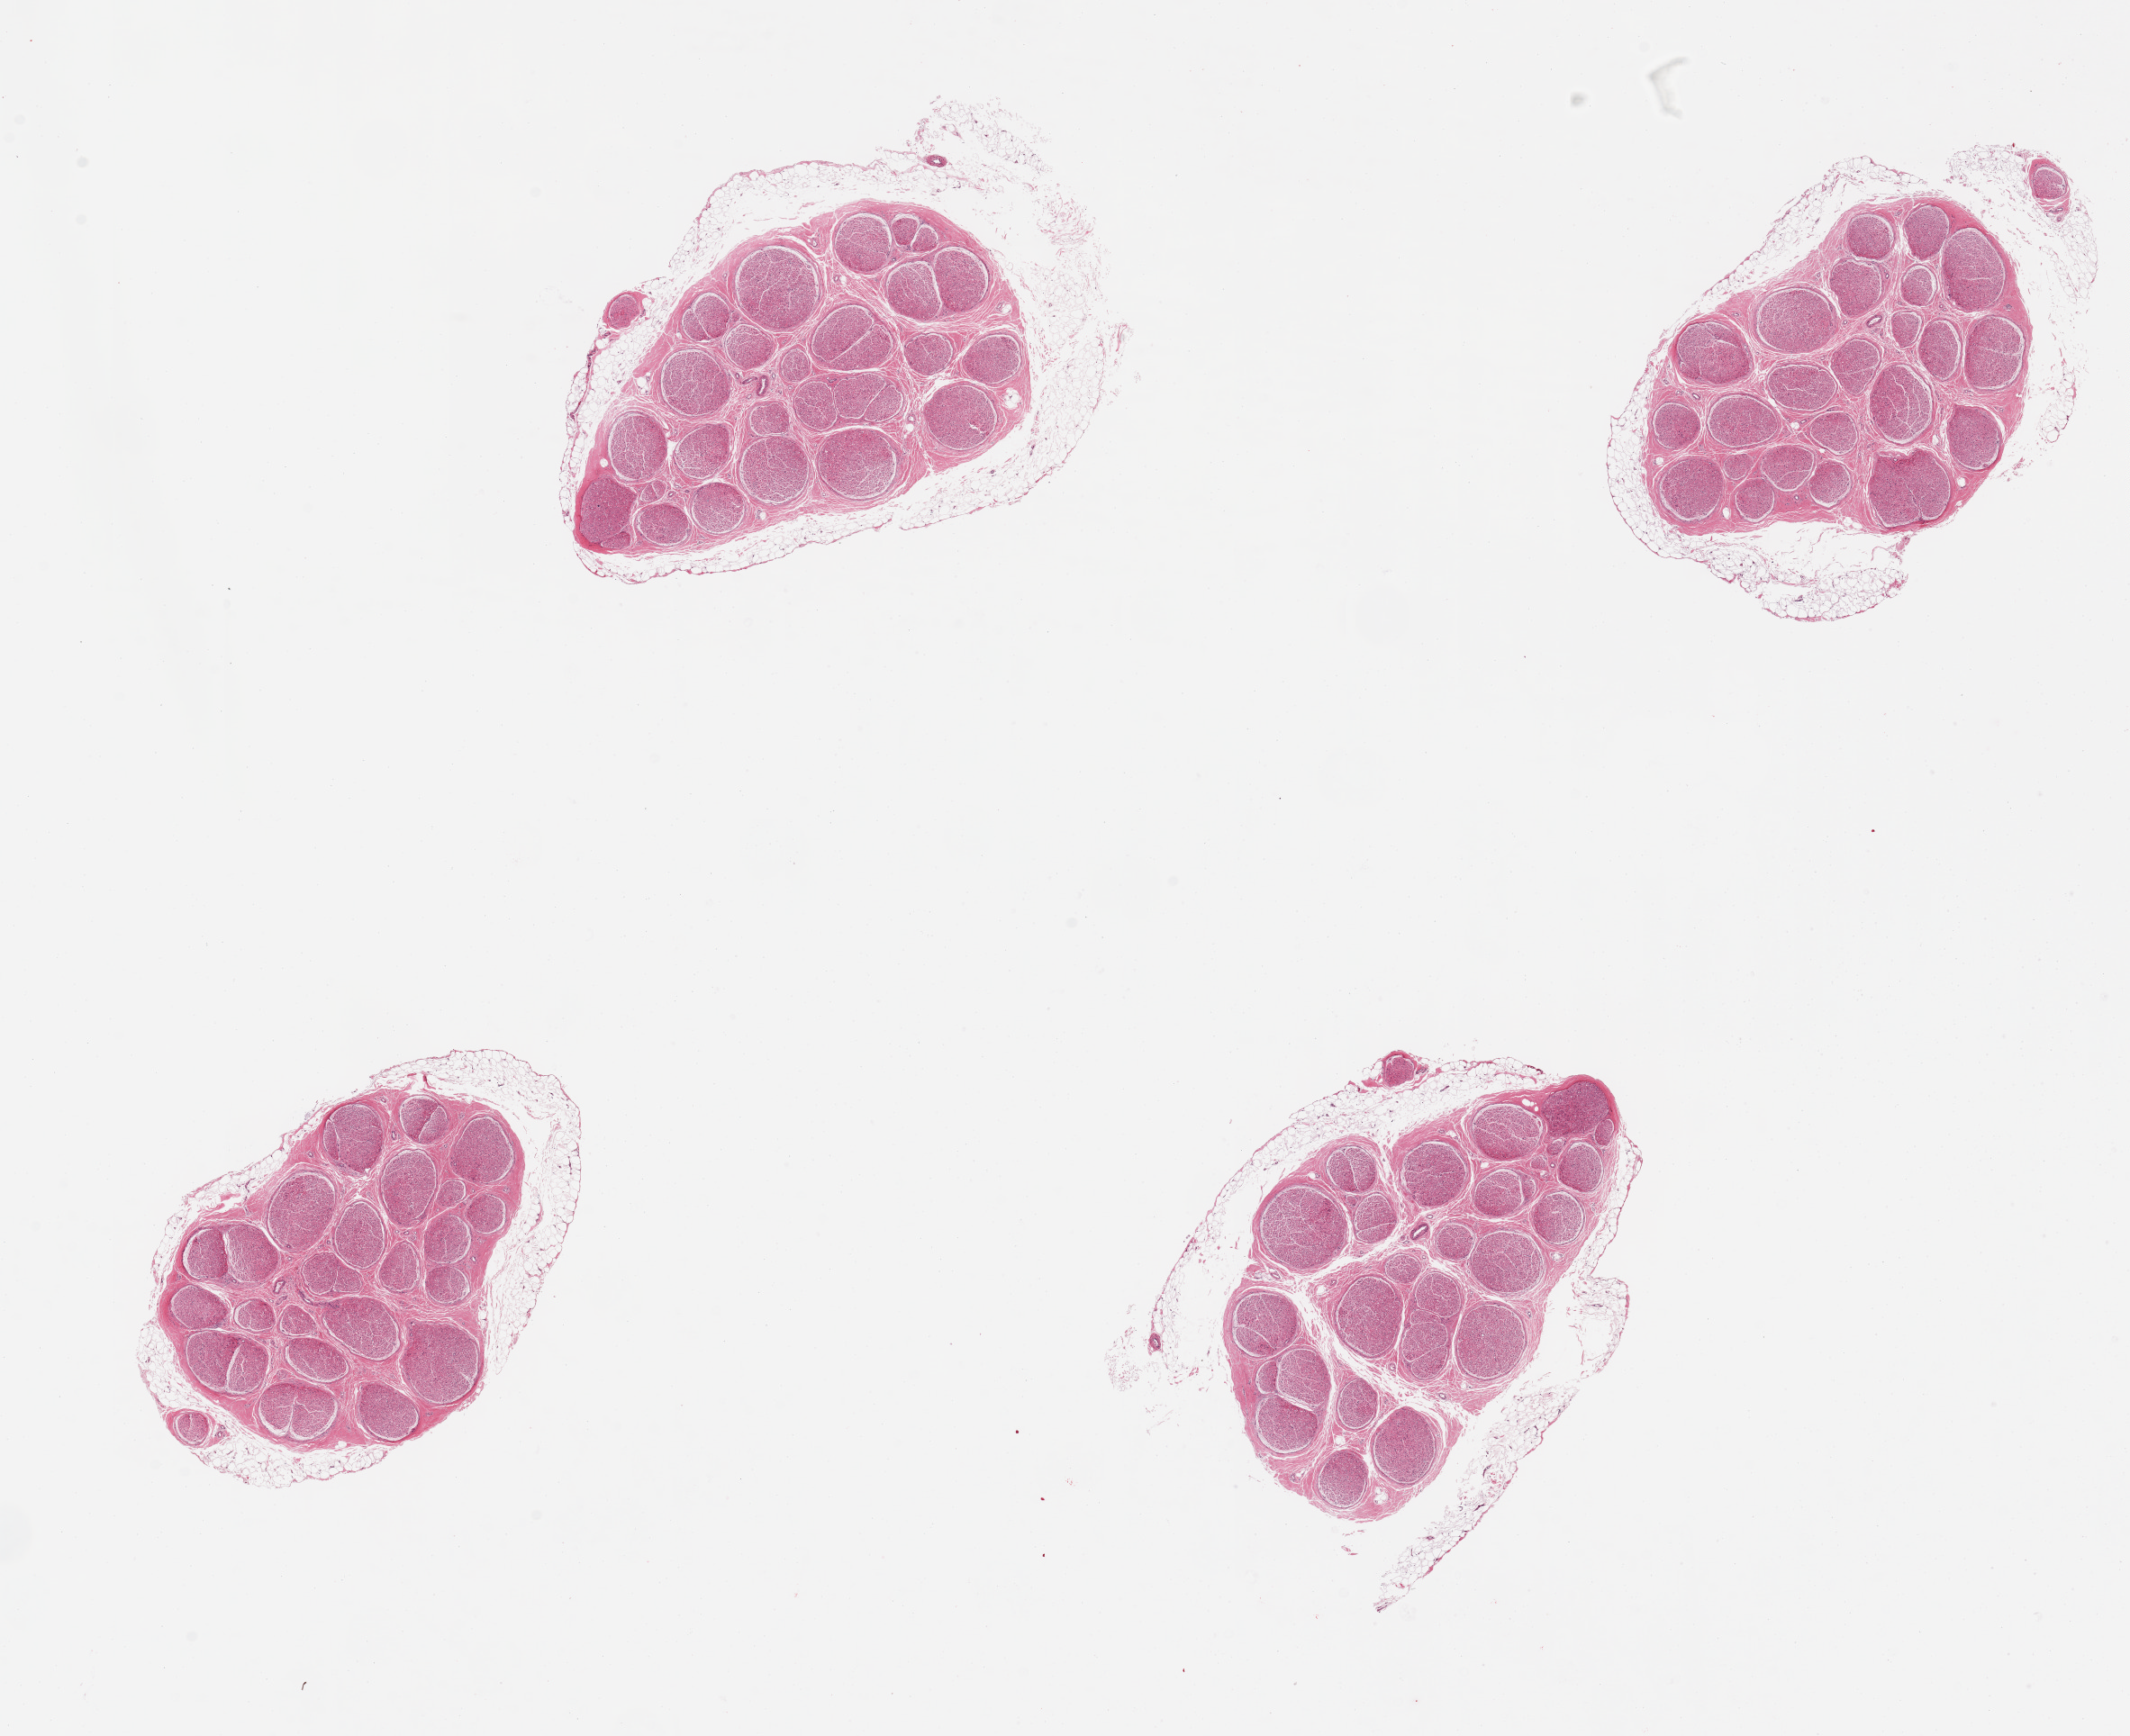
Digitized haematoxylin and eosin-stained section, brightfield, whole scanned area (about 18.7 x 15.2 mm, slide scanned at 20x) shown as a low-resolution overview; PAXgene-fixed, paraffin-embedded tissue; sampled site (target tissue): tibial nerve; tissue donor sample. Donor sex: female.
Reviewer comment on this tissue sample: 4 pieces, rim adherent fat, ~0.5mm.